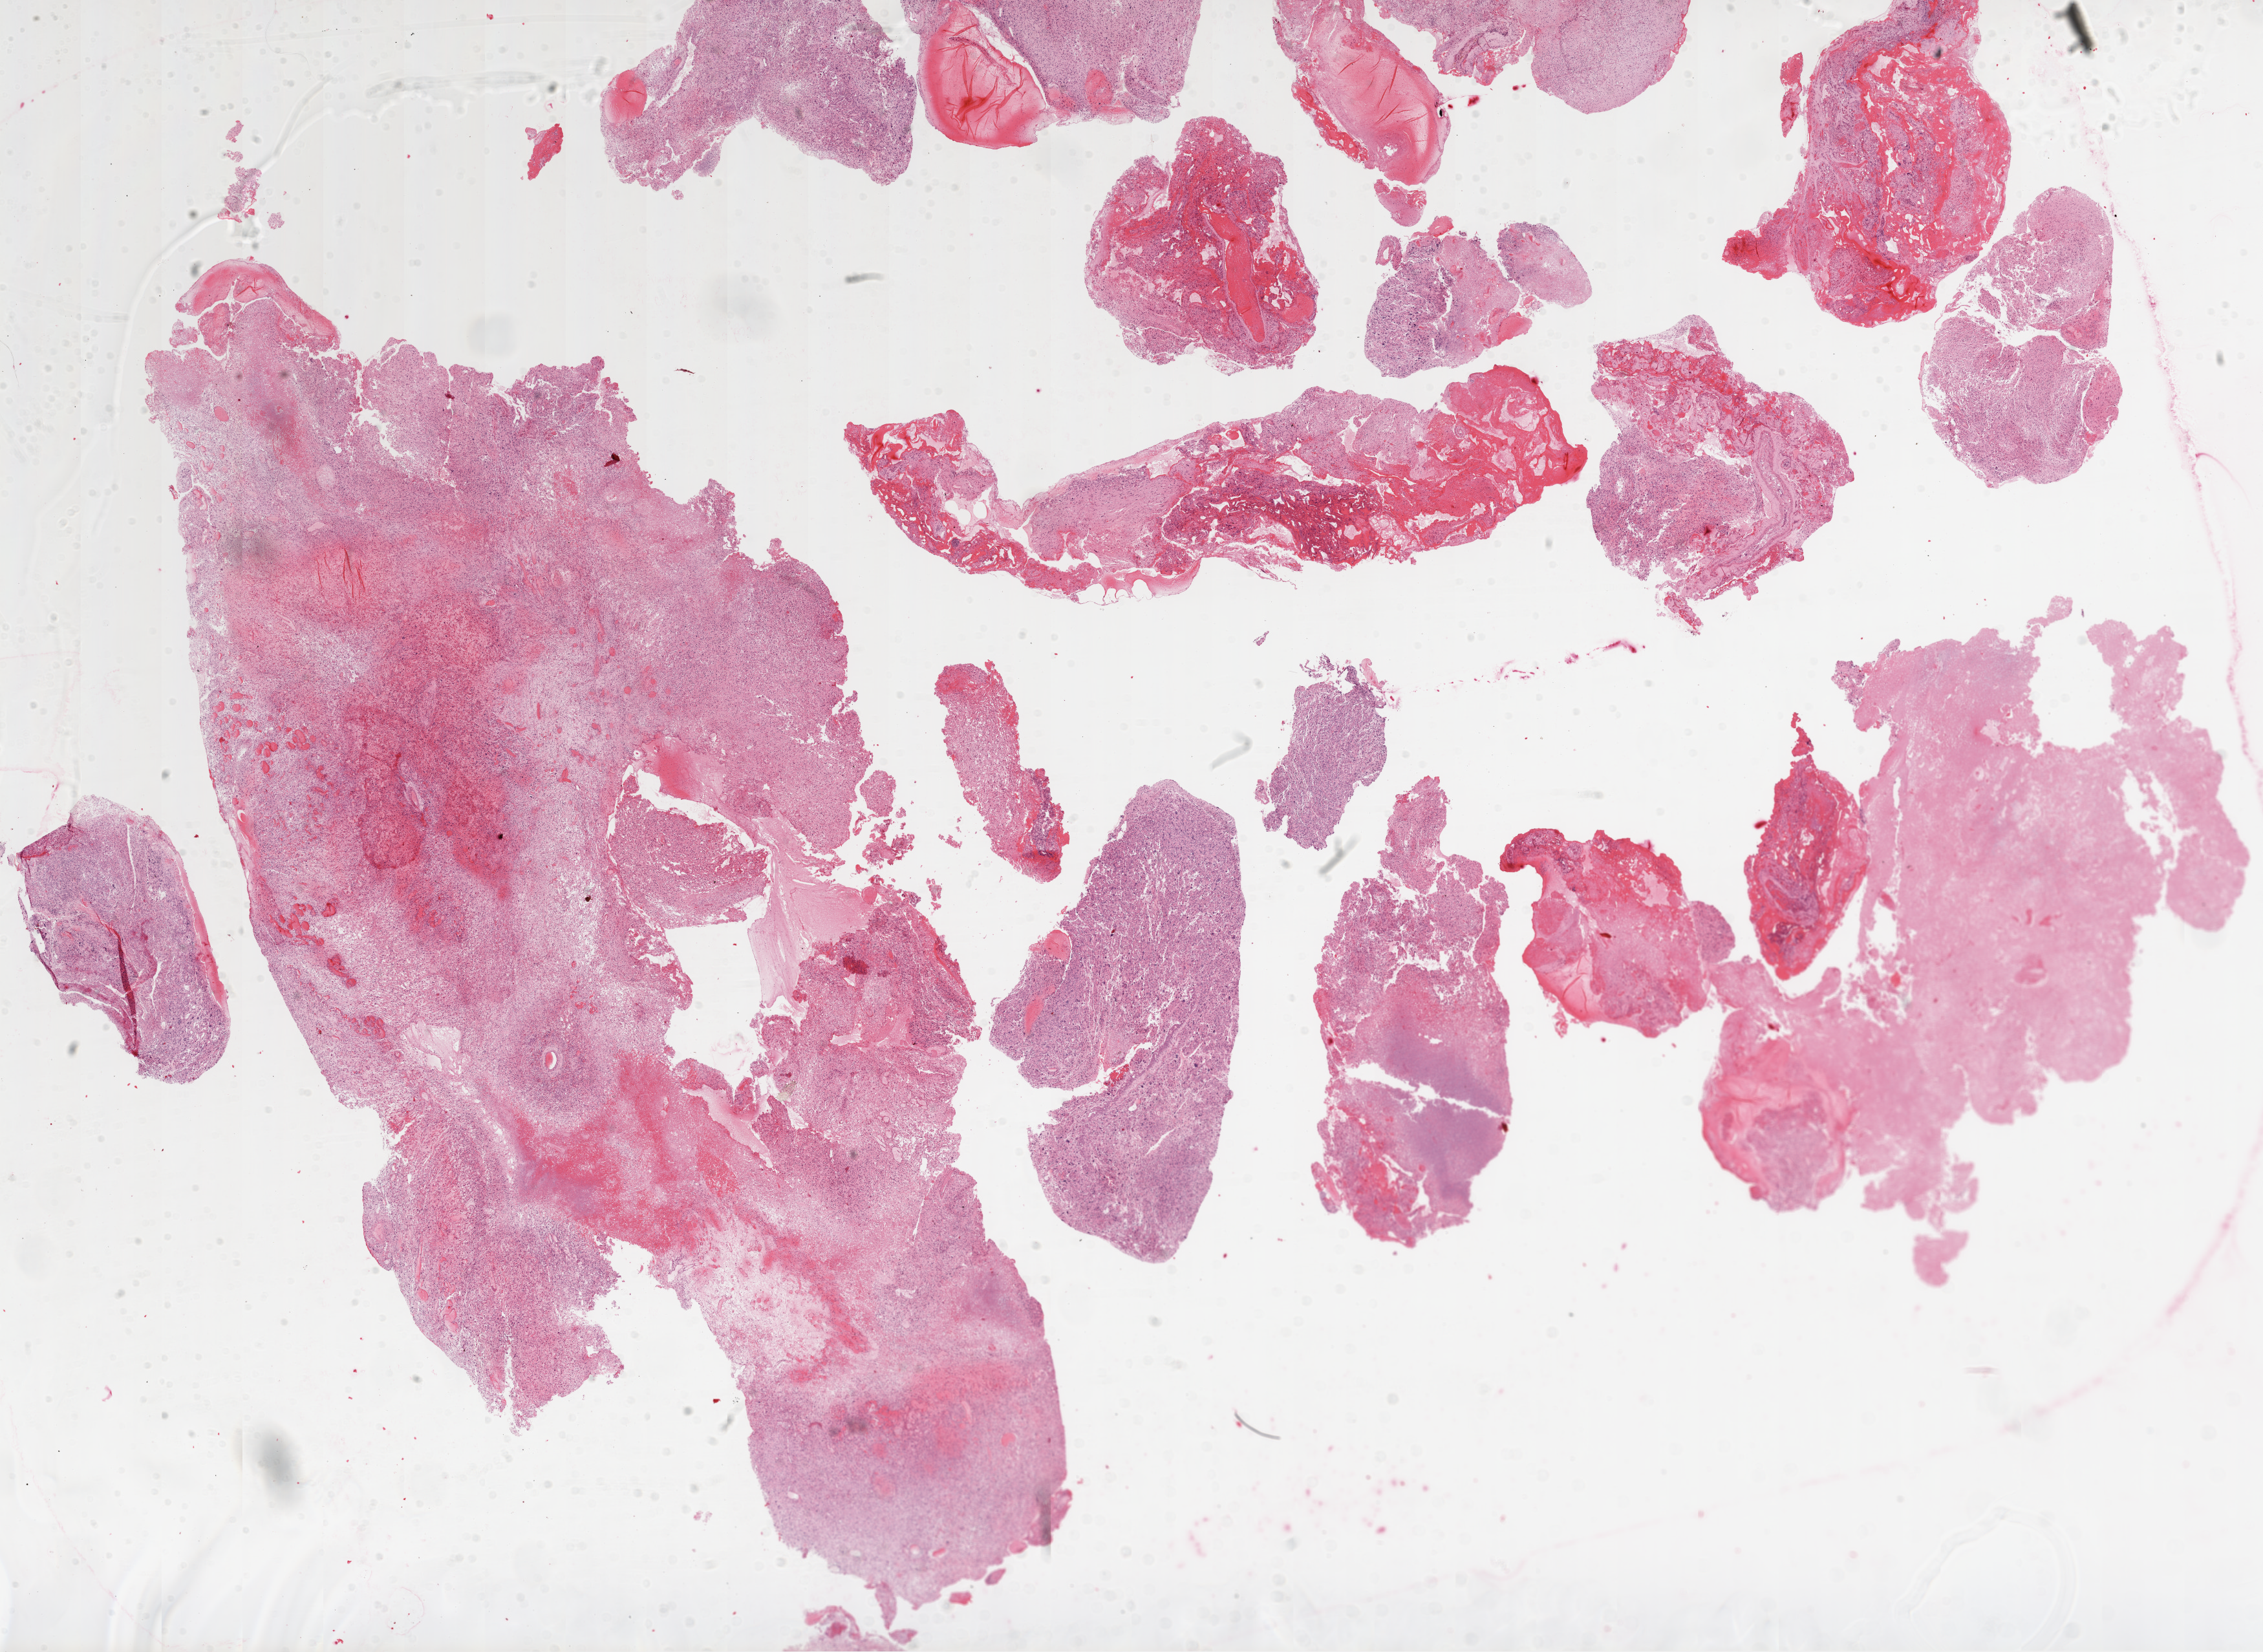
Whole-slide histology image, Hematoxylin and eosin (H&E) stained — low-resolution overview of the scanned area, about 28.1 x 20.5 mm. FFPE section. Brain, primary tumour sample. Female, age 53 years at initial diagnosis.
- histologic diagnosis: Glioblastoma